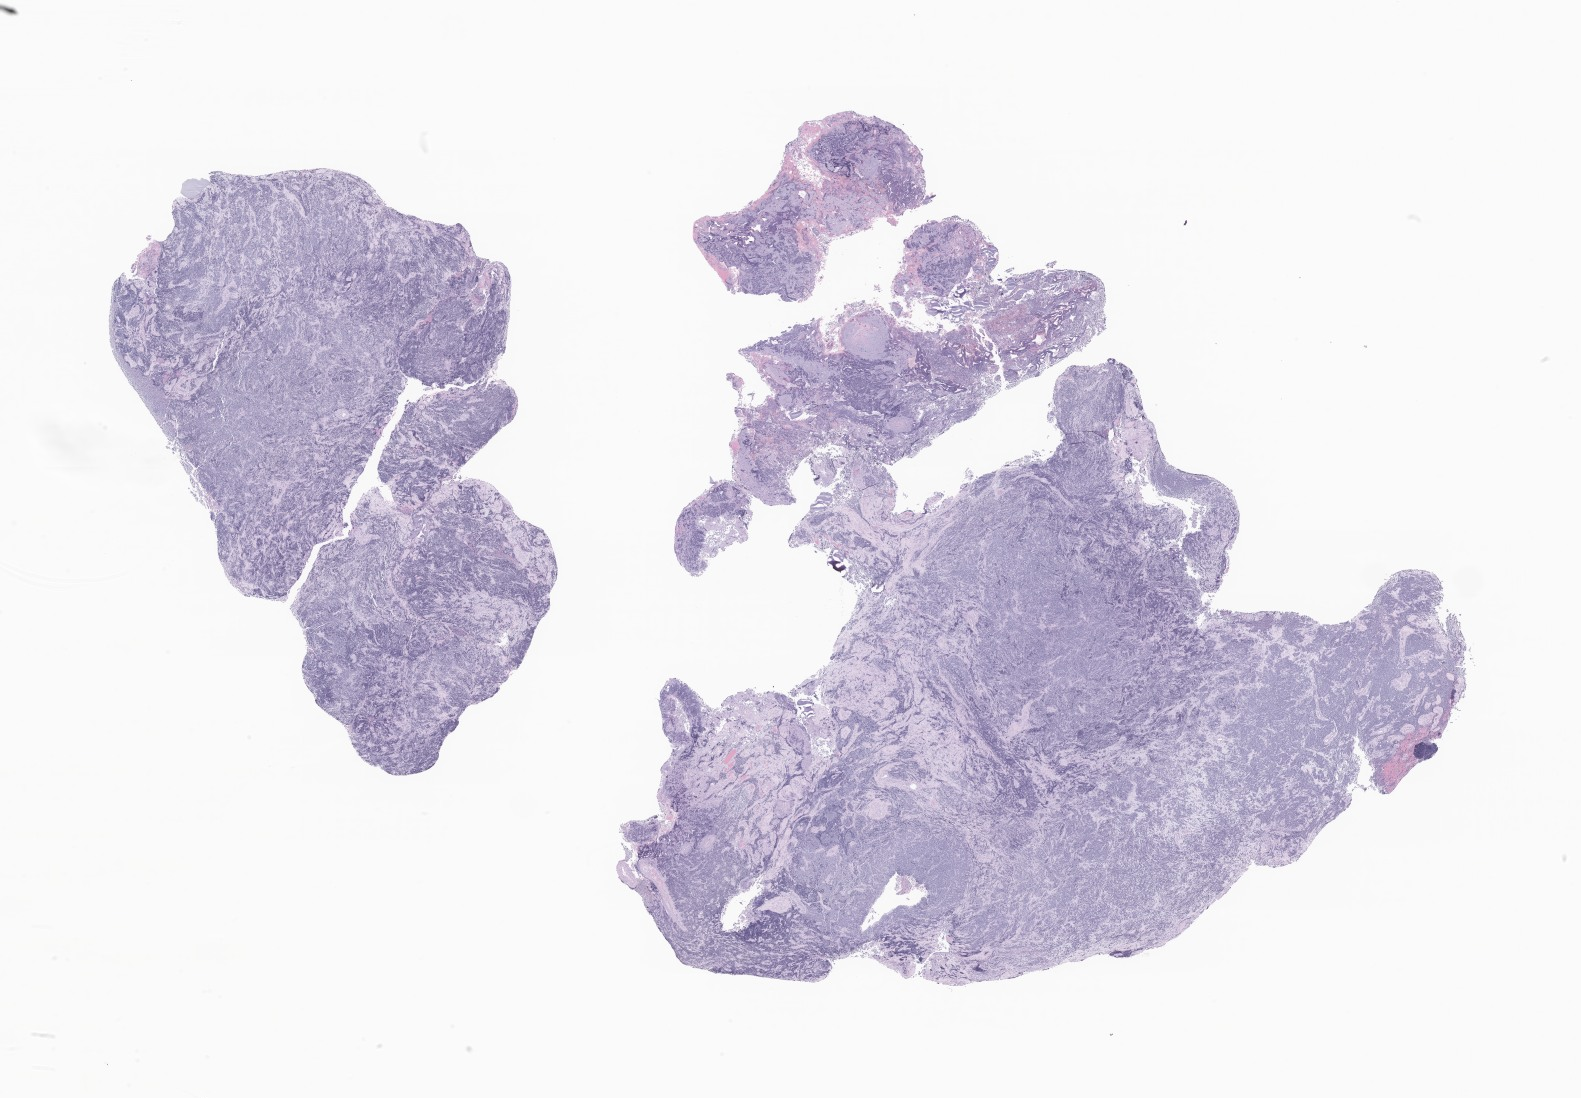
H&E whole-slide image of tumor tissue from the brain — low-resolution overview of the scanned area, about 26.7 x 18.5 mm; formalin-fixed paraffin-embedded section. Patient: female, age 38 months.
Recorded diagnosis: Medulloblastoma, NOS.